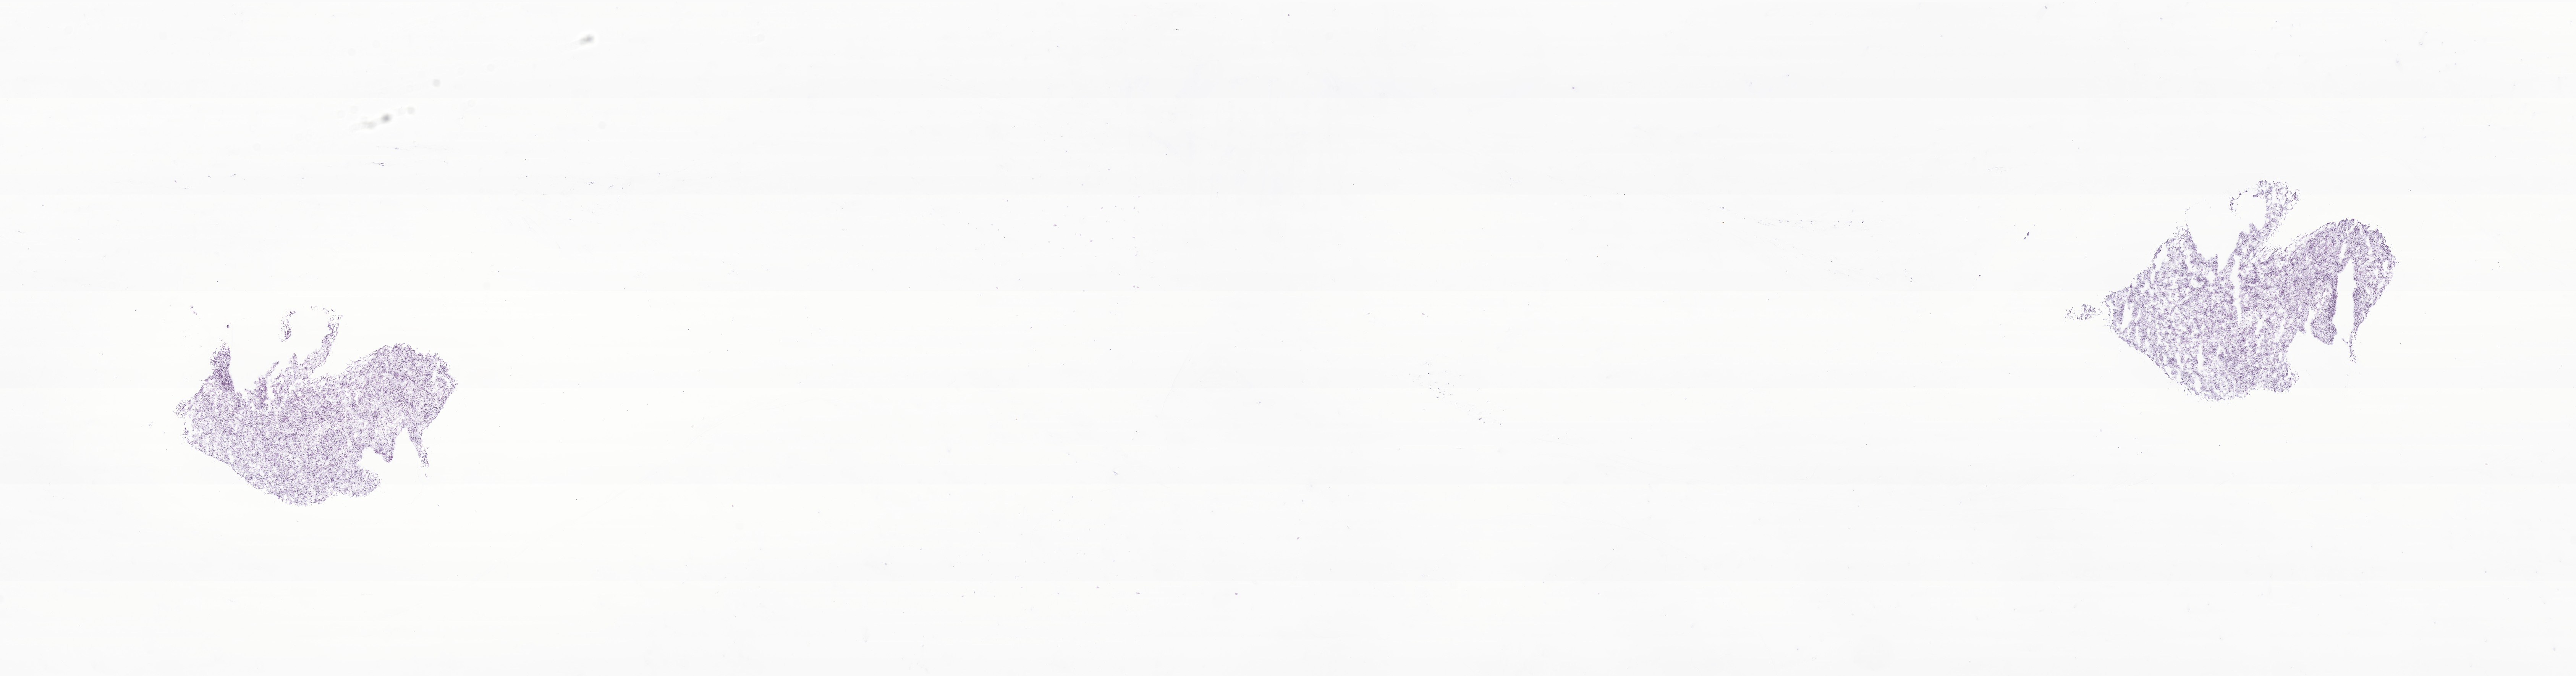
Digitized hematoxylin and eosin (H&E)-stained section of tumor tissue from the spinal cord, whole scanned area (about 28.4 x 7.5 mm) shown as a low-resolution overview, frozen section (OCT-embedded). Patient: male, age 153 months (12 years 9 months).
Diagnosis (ICD-O-3 morphology term): Glioma, malignant.